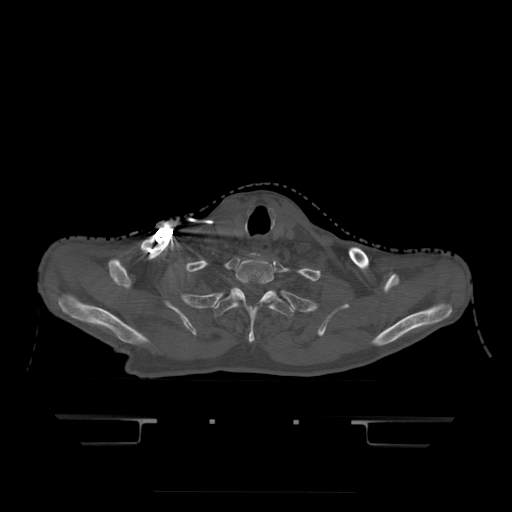
CT including the spine, one axial slice. Bone window (W 1800 / L 400 HU). 512 × 512 image matrix, field of view 436 × 436 mm. Patient age 68 years. Case-level facts recorded for this patient, not image findings: primary cancer: urothelial.
Annotated regions visible in this slice (semi-automatically segmented with operator editing):
- T1 vertebra: box from (x=236, y=259) to (x=277, y=296) px
- T2 vertebra: (x=214, y=288)–(x=294, y=344)